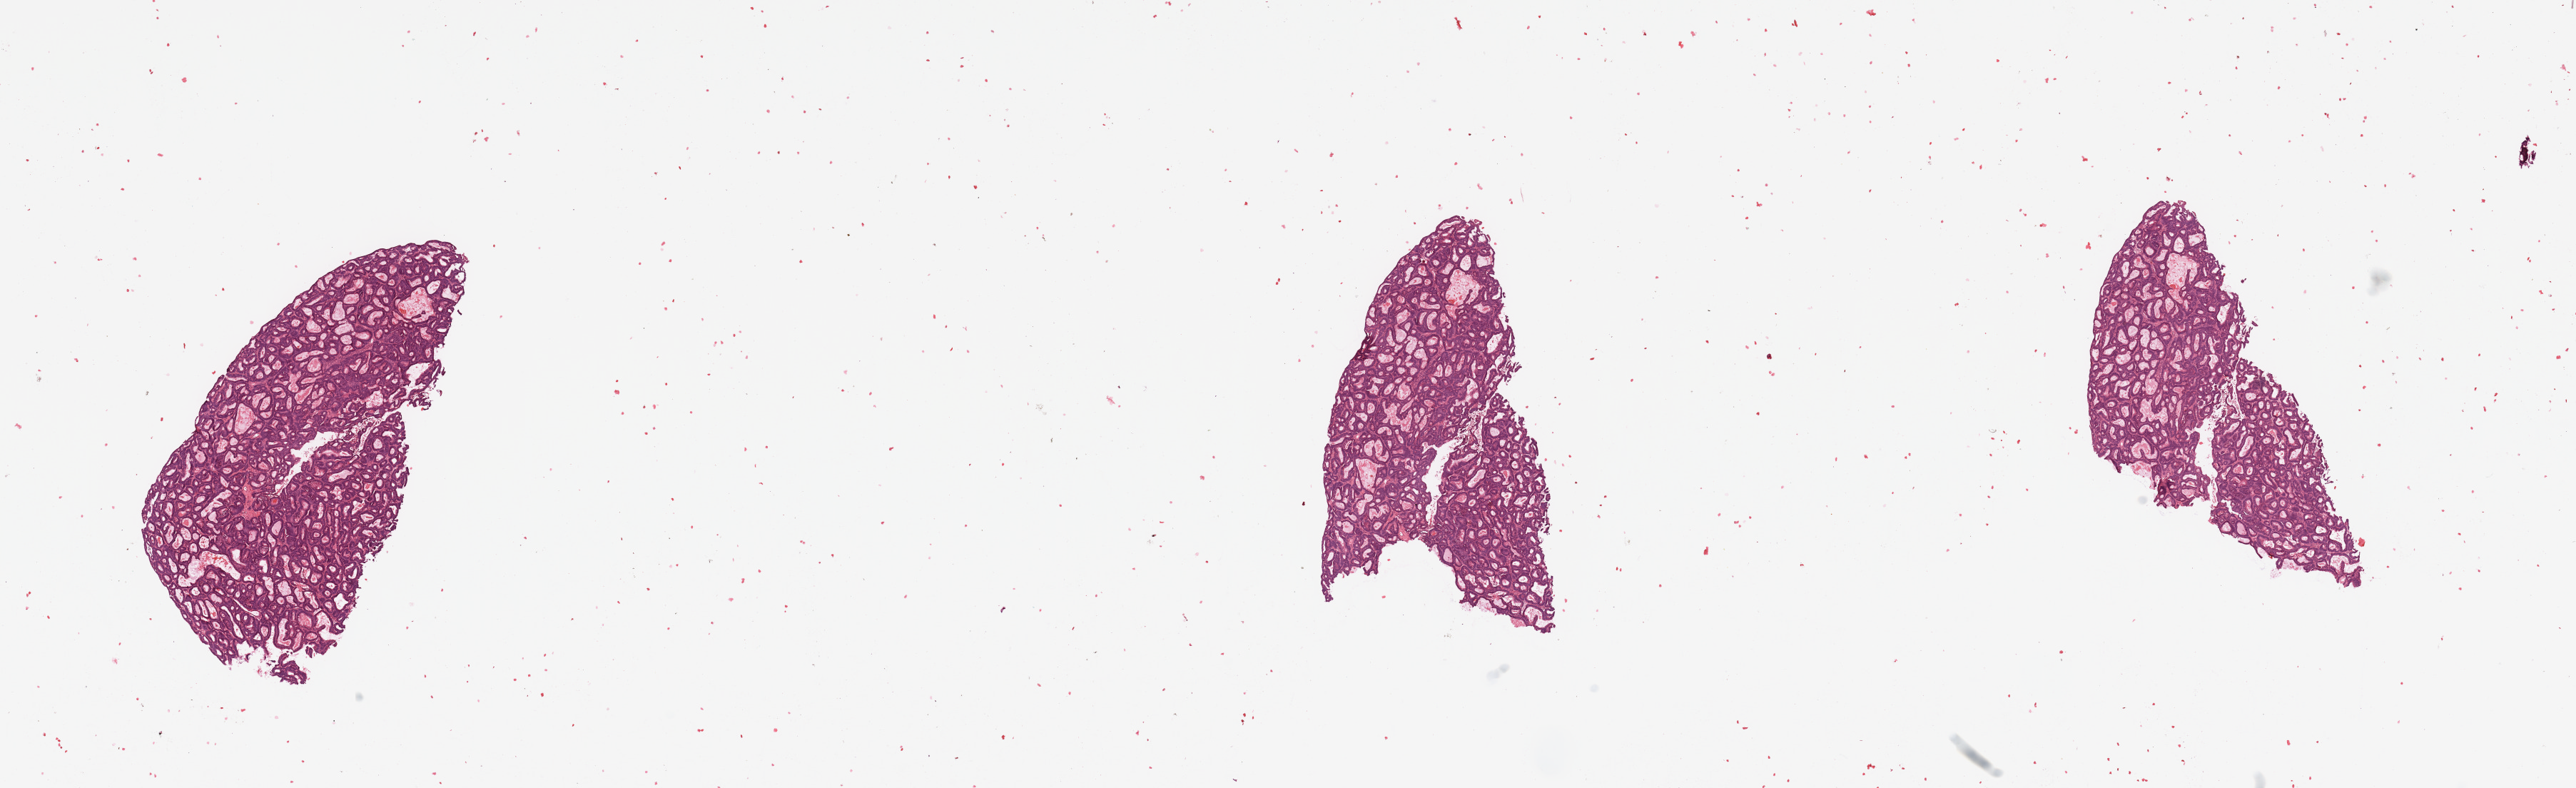
Whole-slide histology image, Hematoxylin and eosin (H&E) stained, shown as a low-resolution overview of the whole scanned area (about 28.5 x 8.7 mm, from a 20x scan), tumour tissue sample, sampled site: uterus. 84-year-old female patient. Slide review estimates, as recorded: tumour nuclei 90%, necrosis 0%.
Histologic diagnosis: Endometrioid adenocarcinoma, NOS.